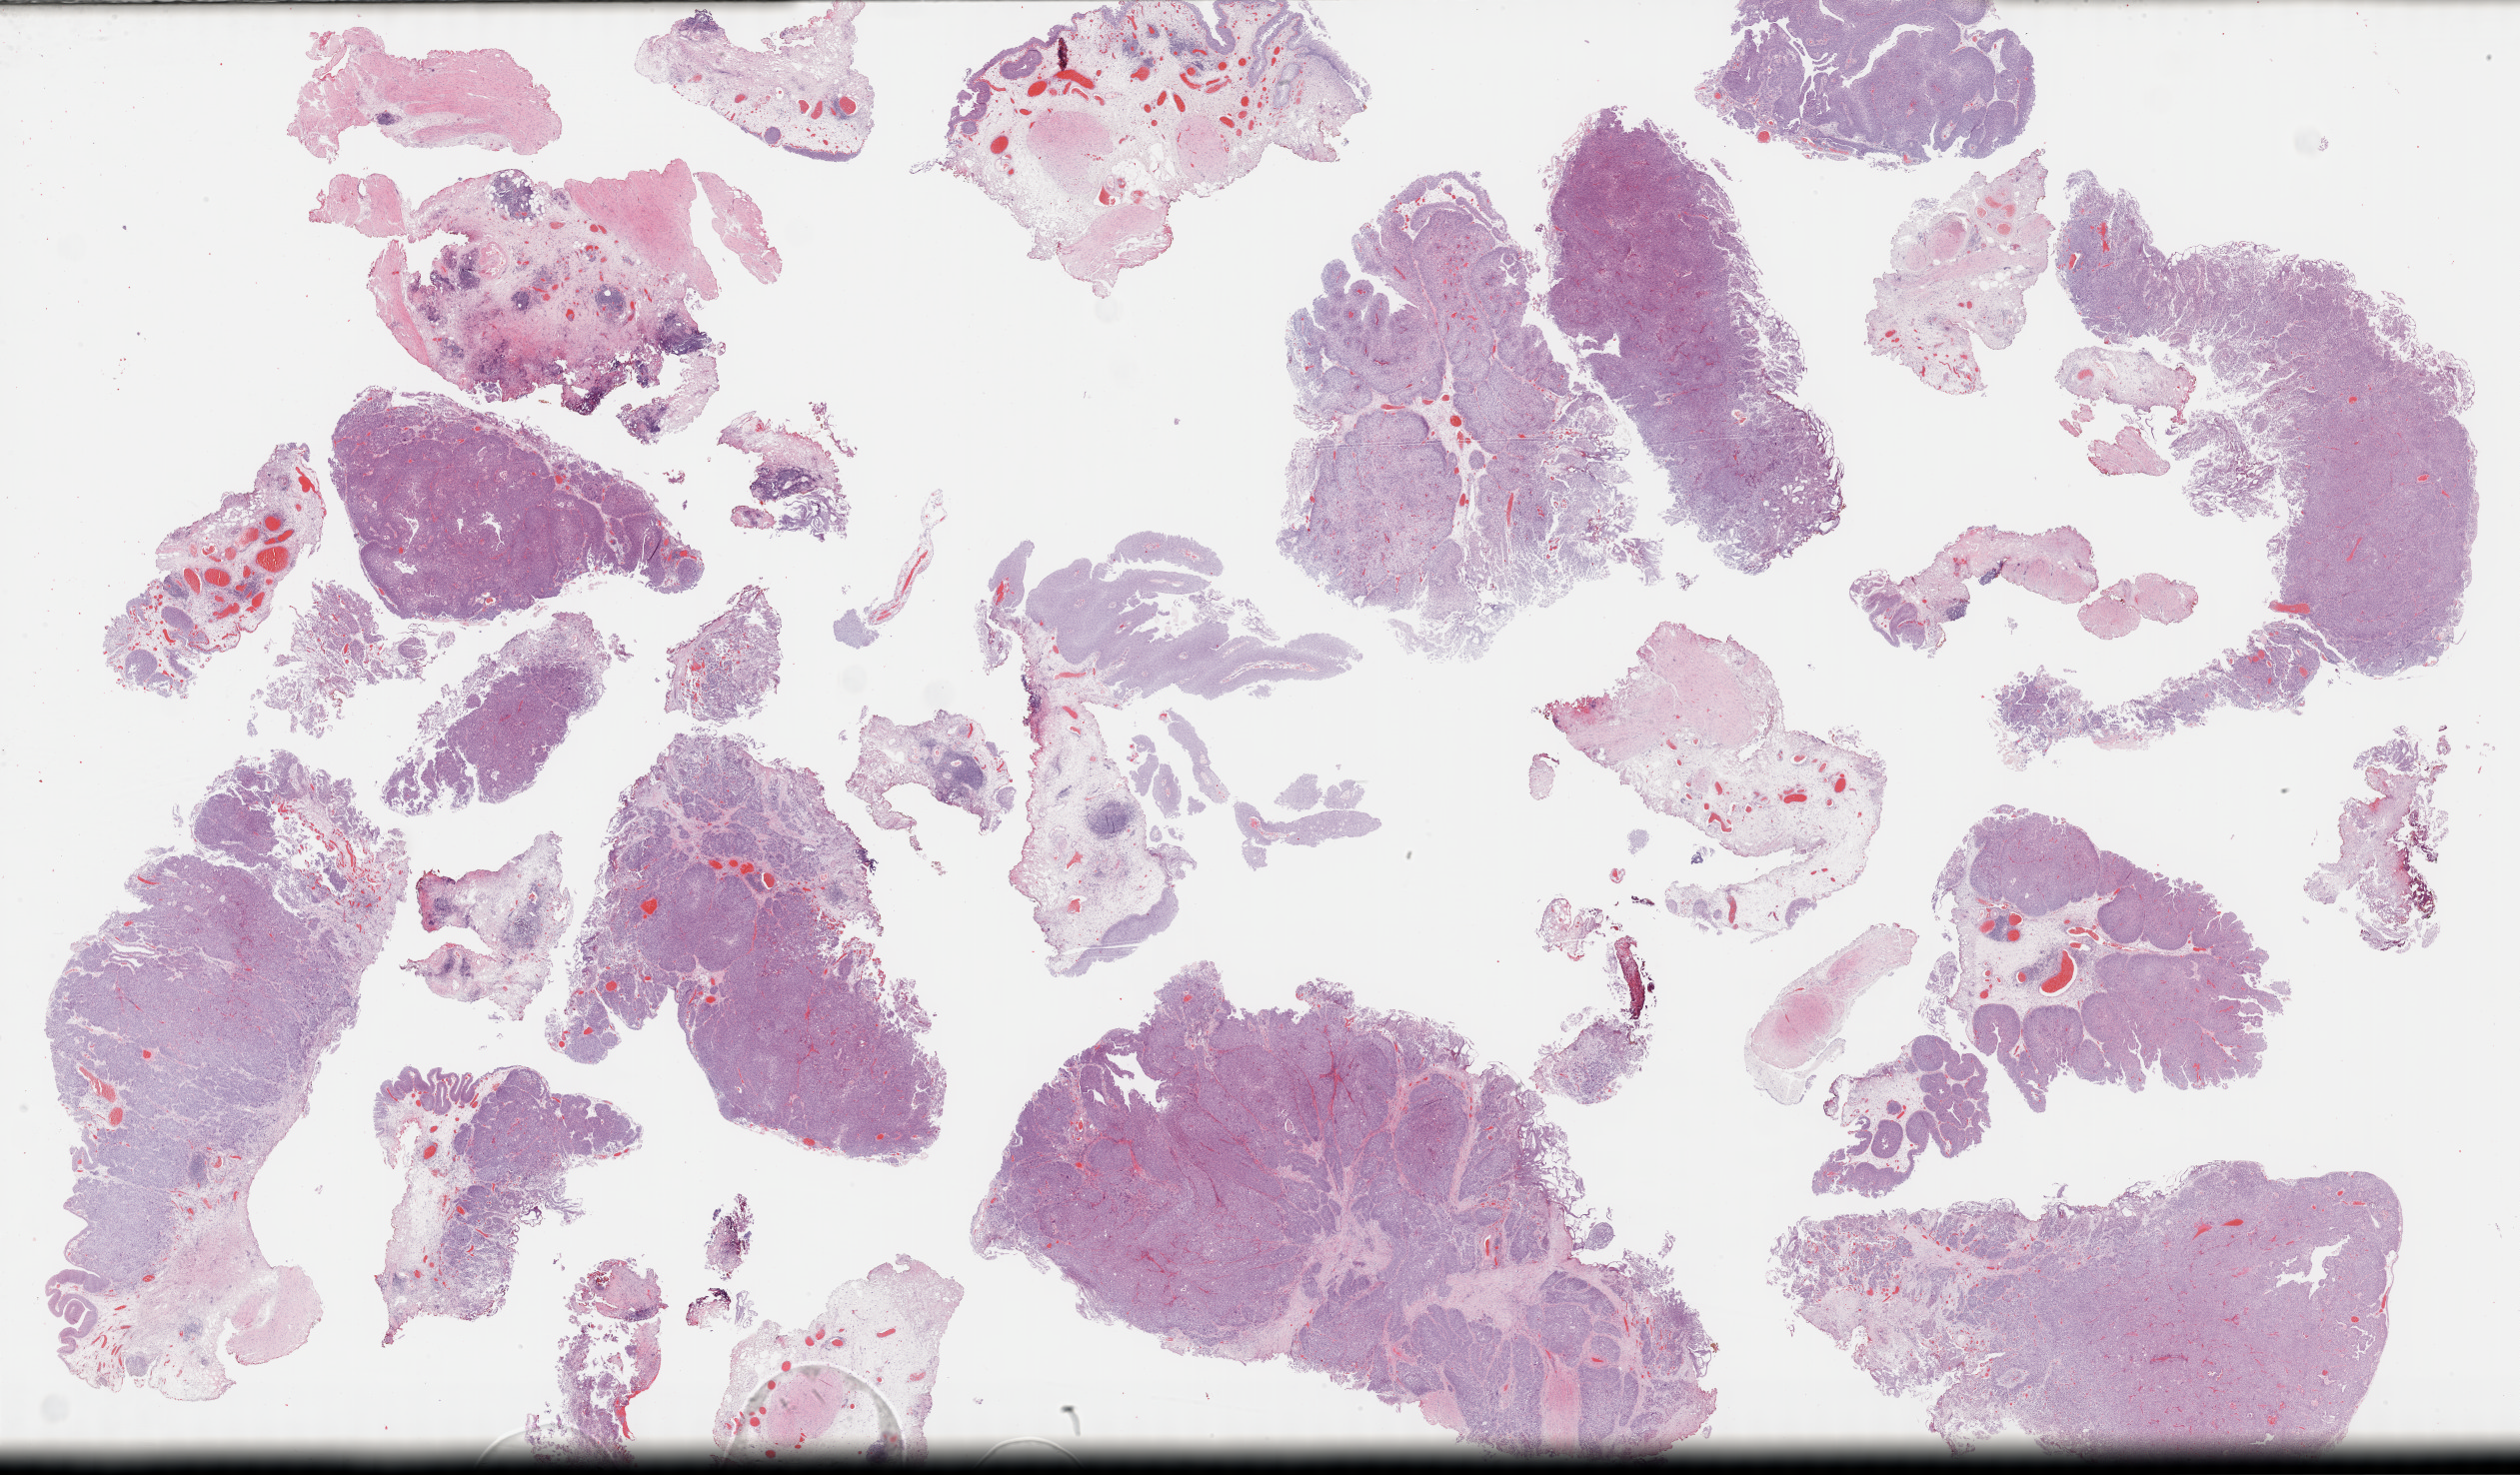
Digitized H&E-stained tissue section (whole slide), a low-resolution overview of the entire scanned area, about 40.8 x 23.9 mm (slide scanned at 40x). Formalin-fixed paraffin-embedded (FFPE) diagnostic section. Sample: primary tumour, bladder. Patient: male, age at initial diagnosis 70 years. Histologic grade: high grade.
* diagnosis: Transitional cell carcinoma
* TNM: T0 N0 MX
* AJCC pathologic stage: II